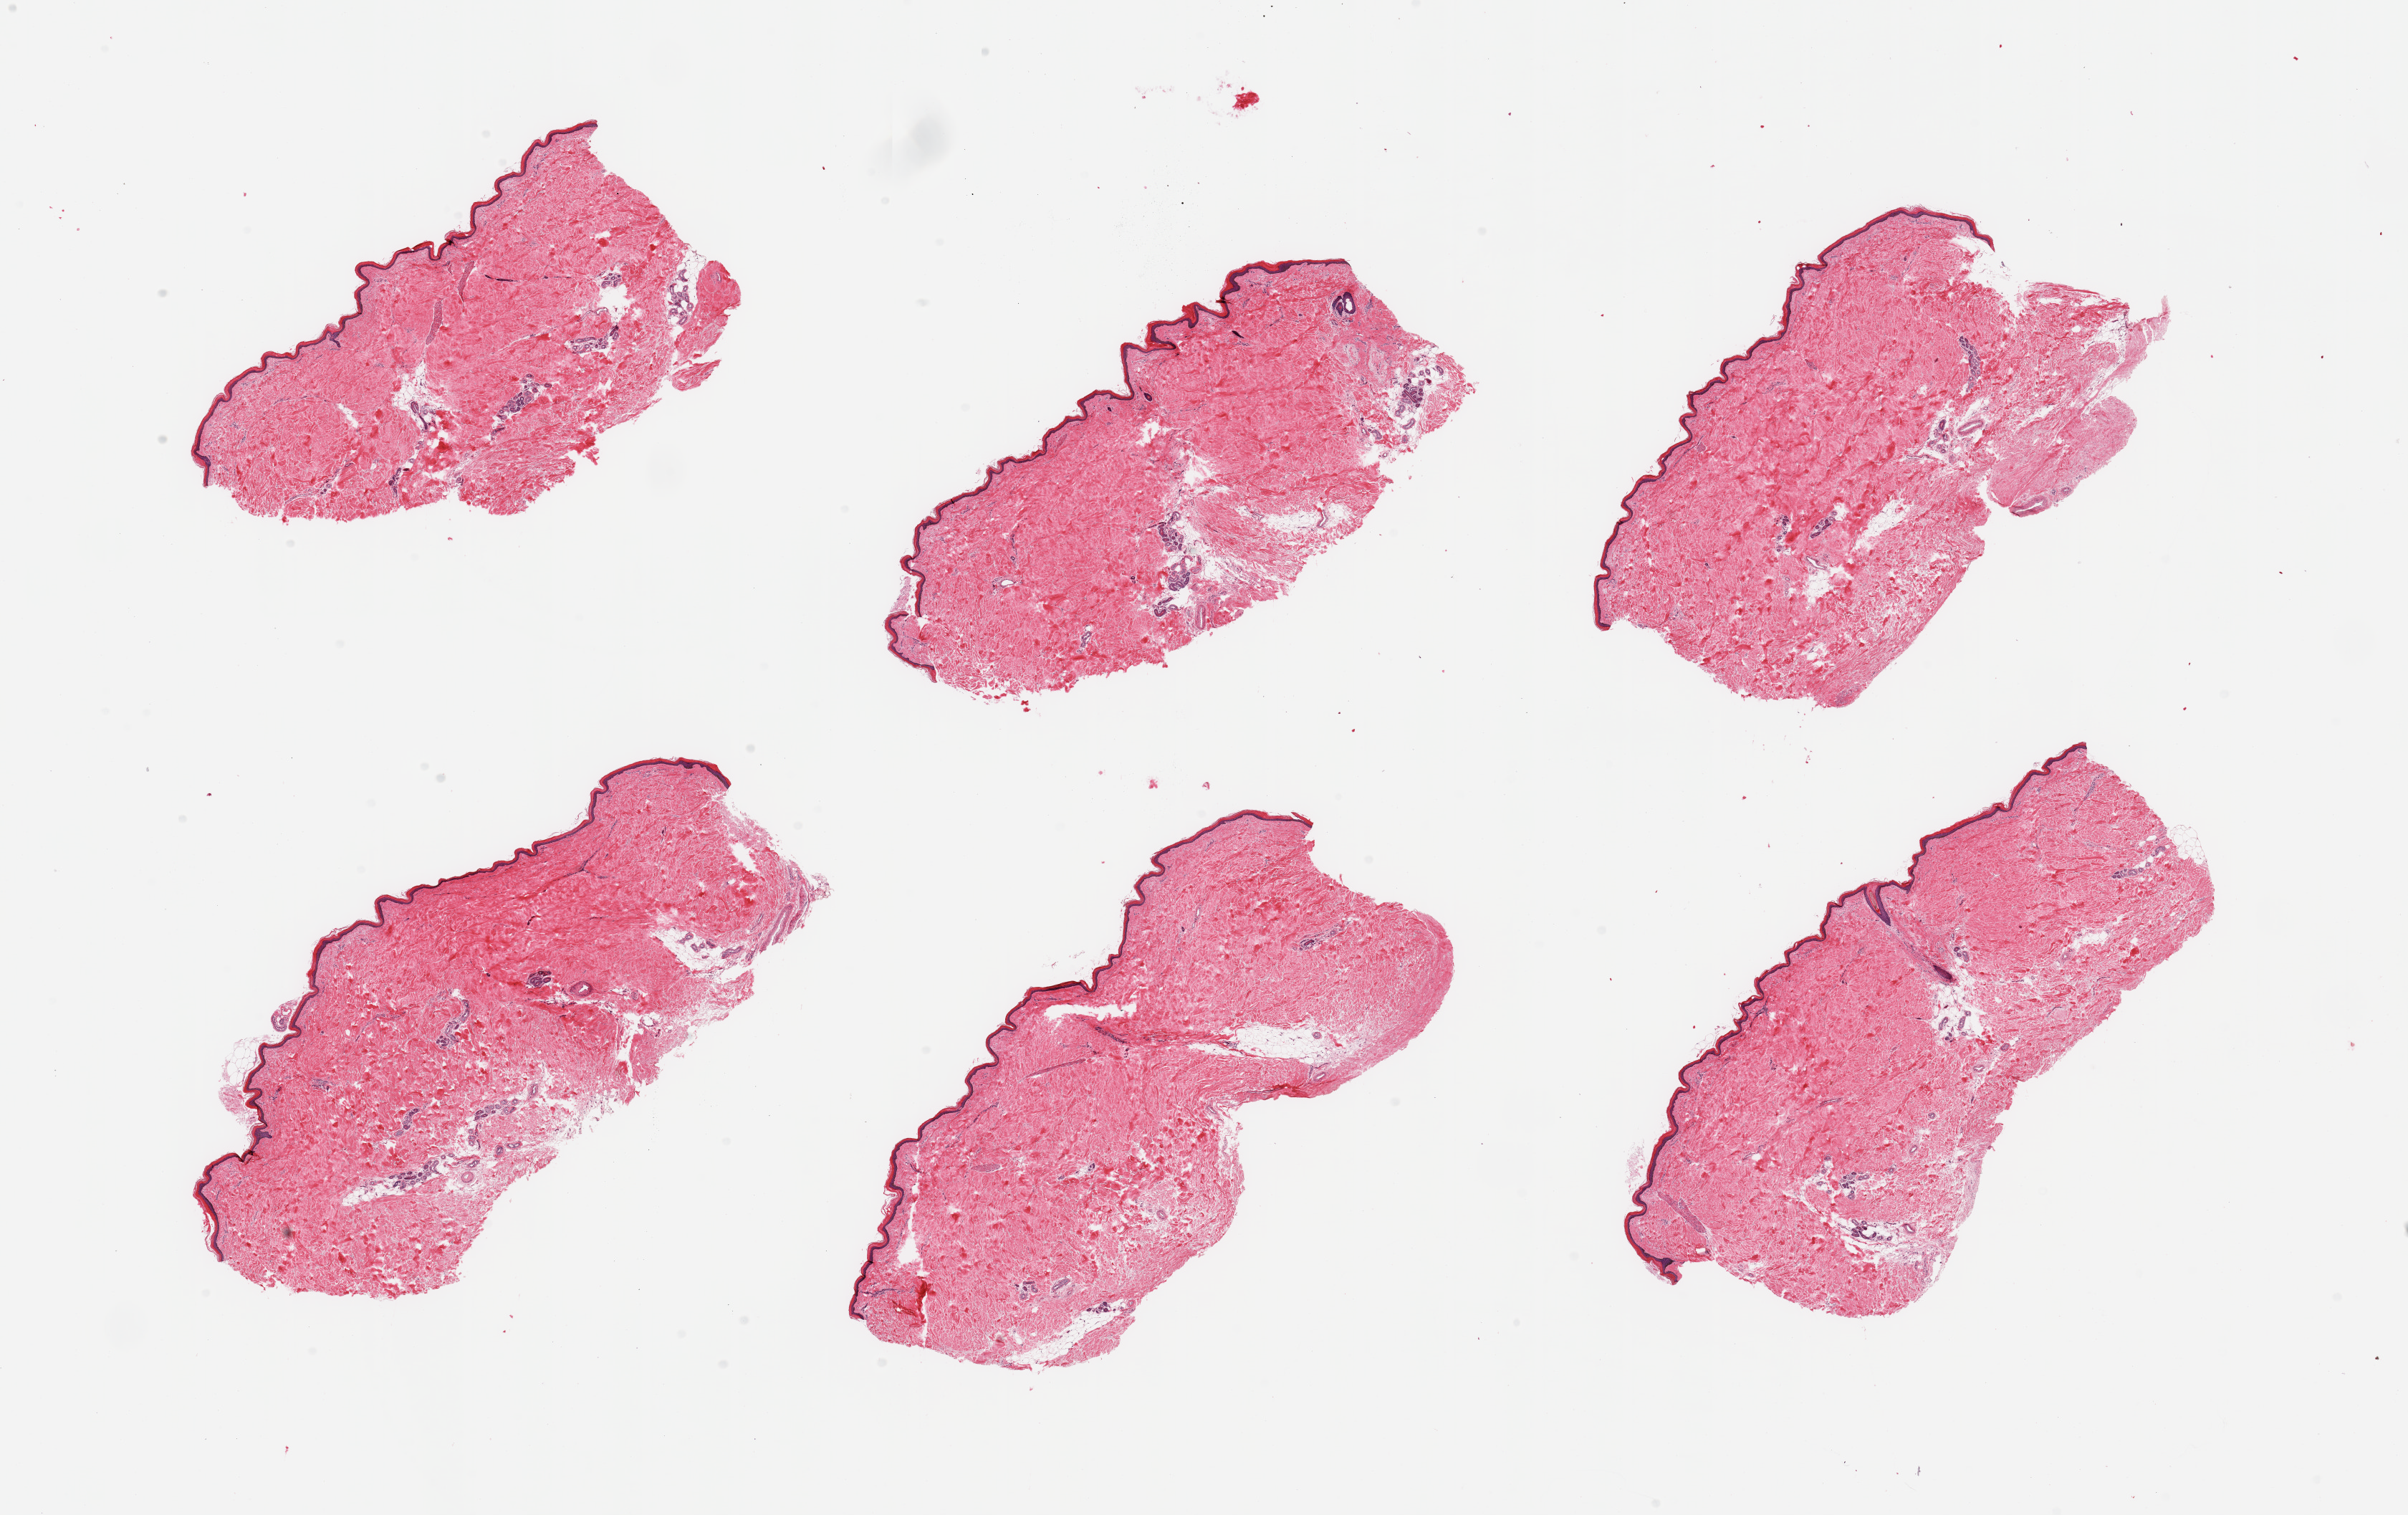
Digitized haematoxylin and eosin-stained section, brightfield — whole scanned area (about 26.6 x 16.7 mm) shown as a low-resolution overview. PAXgene-fixed paraffin-embedded (PFPE) section. Target tissue: skin of lower leg. Donor tissue sample. Donor sex: male.
Pathologist's review note for this sample: 6 pieces, no dermal fat; squamous epithelium is ~20-30 microns.